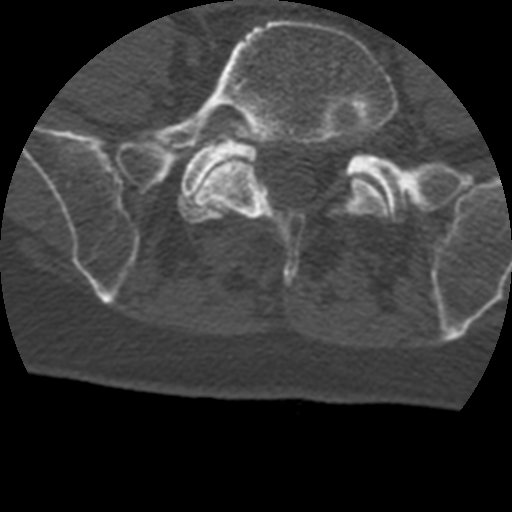
CT including the spine, one axial slice. Position 37 of 399 along the scan axis. Reconstruction kernel STANDARD. Bone window (W 1800 / L 400 HU). 1.25 mm slice thickness. 512 × 512 image matrix, field of view 160 × 160 mm. Patient age 69 years. Case-level facts recorded for this patient, not image findings: primary cancer: prostate.
Annotated regions visible in this slice (semi-automatic segmentation, software-assisted and operator-edited):
- L5 vertebra: bounding box [x1, y1, x2, y2] px = [140, 19, 398, 285]